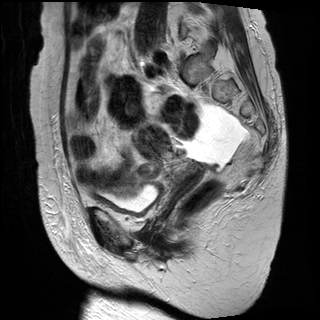
Pelvic MRI for cervical cancer, one sagittal slice. Position 19 of 30 along the scan axis. T2-weighted. 1.5 T. TE 89 ms, TR 2930 ms. 4 mm slice thickness. 320 × 320 image matrix, field of view 260 × 260 mm. Patient: female, 61 years.
Annotated regions visible in this slice (manually delineated by an expert):
- uterus and cervix: box from (x=134, y=125) to (x=204, y=184) px